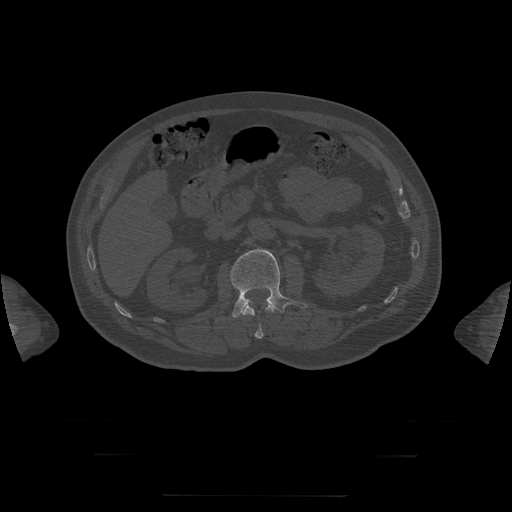
CT including the spine, one axial slice. Slice 31 of 397 in the series (ordered by position). Reconstruction kernel STANDARD. 120 kVp. Bone window (W 1800 / L 400 HU). 512 × 512 image matrix, field of view 510 × 510 mm. Patient age 73 years. Case-level facts recorded for this patient, not image findings: primary cancer: prostate.
Structures marked on this image (semi-automatic segmentation, software-assisted and operator-edited):
- L1 vertebra: box from (x=243, y=301) to (x=275, y=339) px